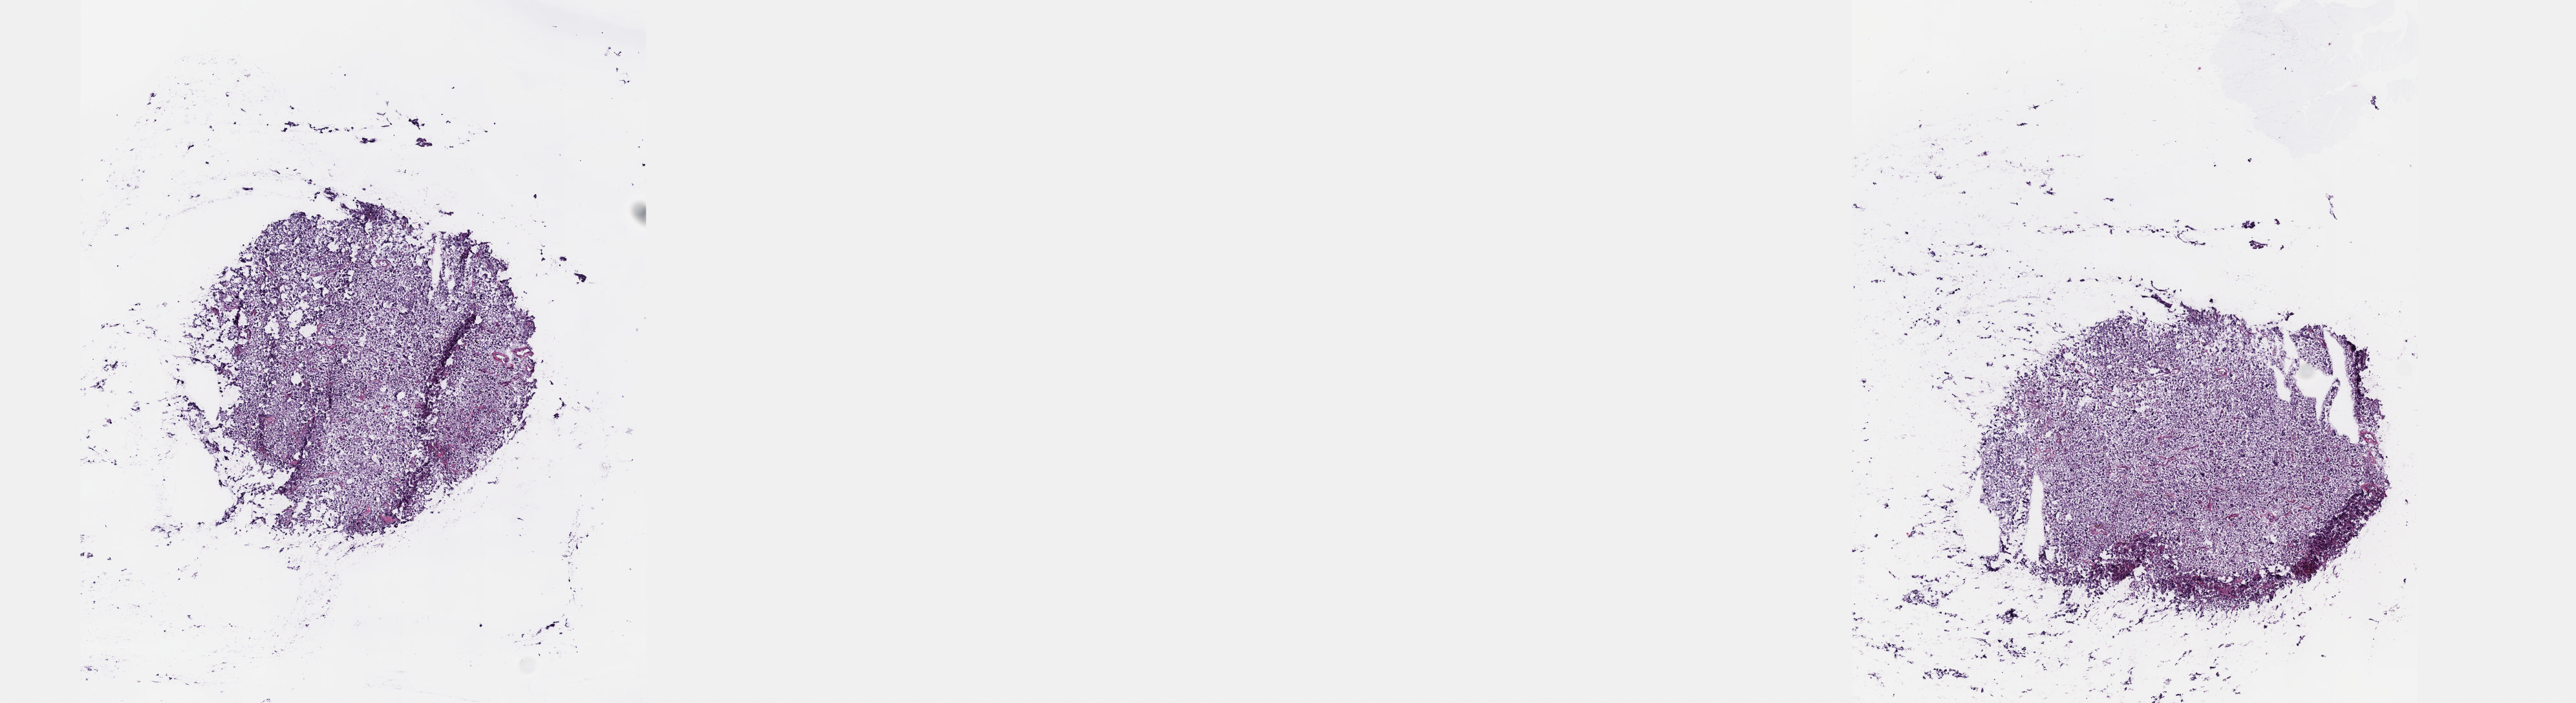
Digitized H&E tissue section (whole slide) — whole scanned area (about 16.1 x 4.4 mm, slide scanned at 40x) shown as a low-resolution overview; frozen section from the top of the tissue portion; adrenal gland, primary tumour sample. Female, age 44 years at initial diagnosis. Pathologist review of this section (percent, as recorded): tumour cells 100%, tumour nuclei 80%, normal cells 0%, stromal cells 0%, necrosis 0%. Inflammatory infiltration, as recorded: lymphocyte infiltration 1%, monocyte infiltration 0%, neutrophil infiltration 0%.
- laterality: right
- histologic diagnosis: Pheochromocytoma, NOS